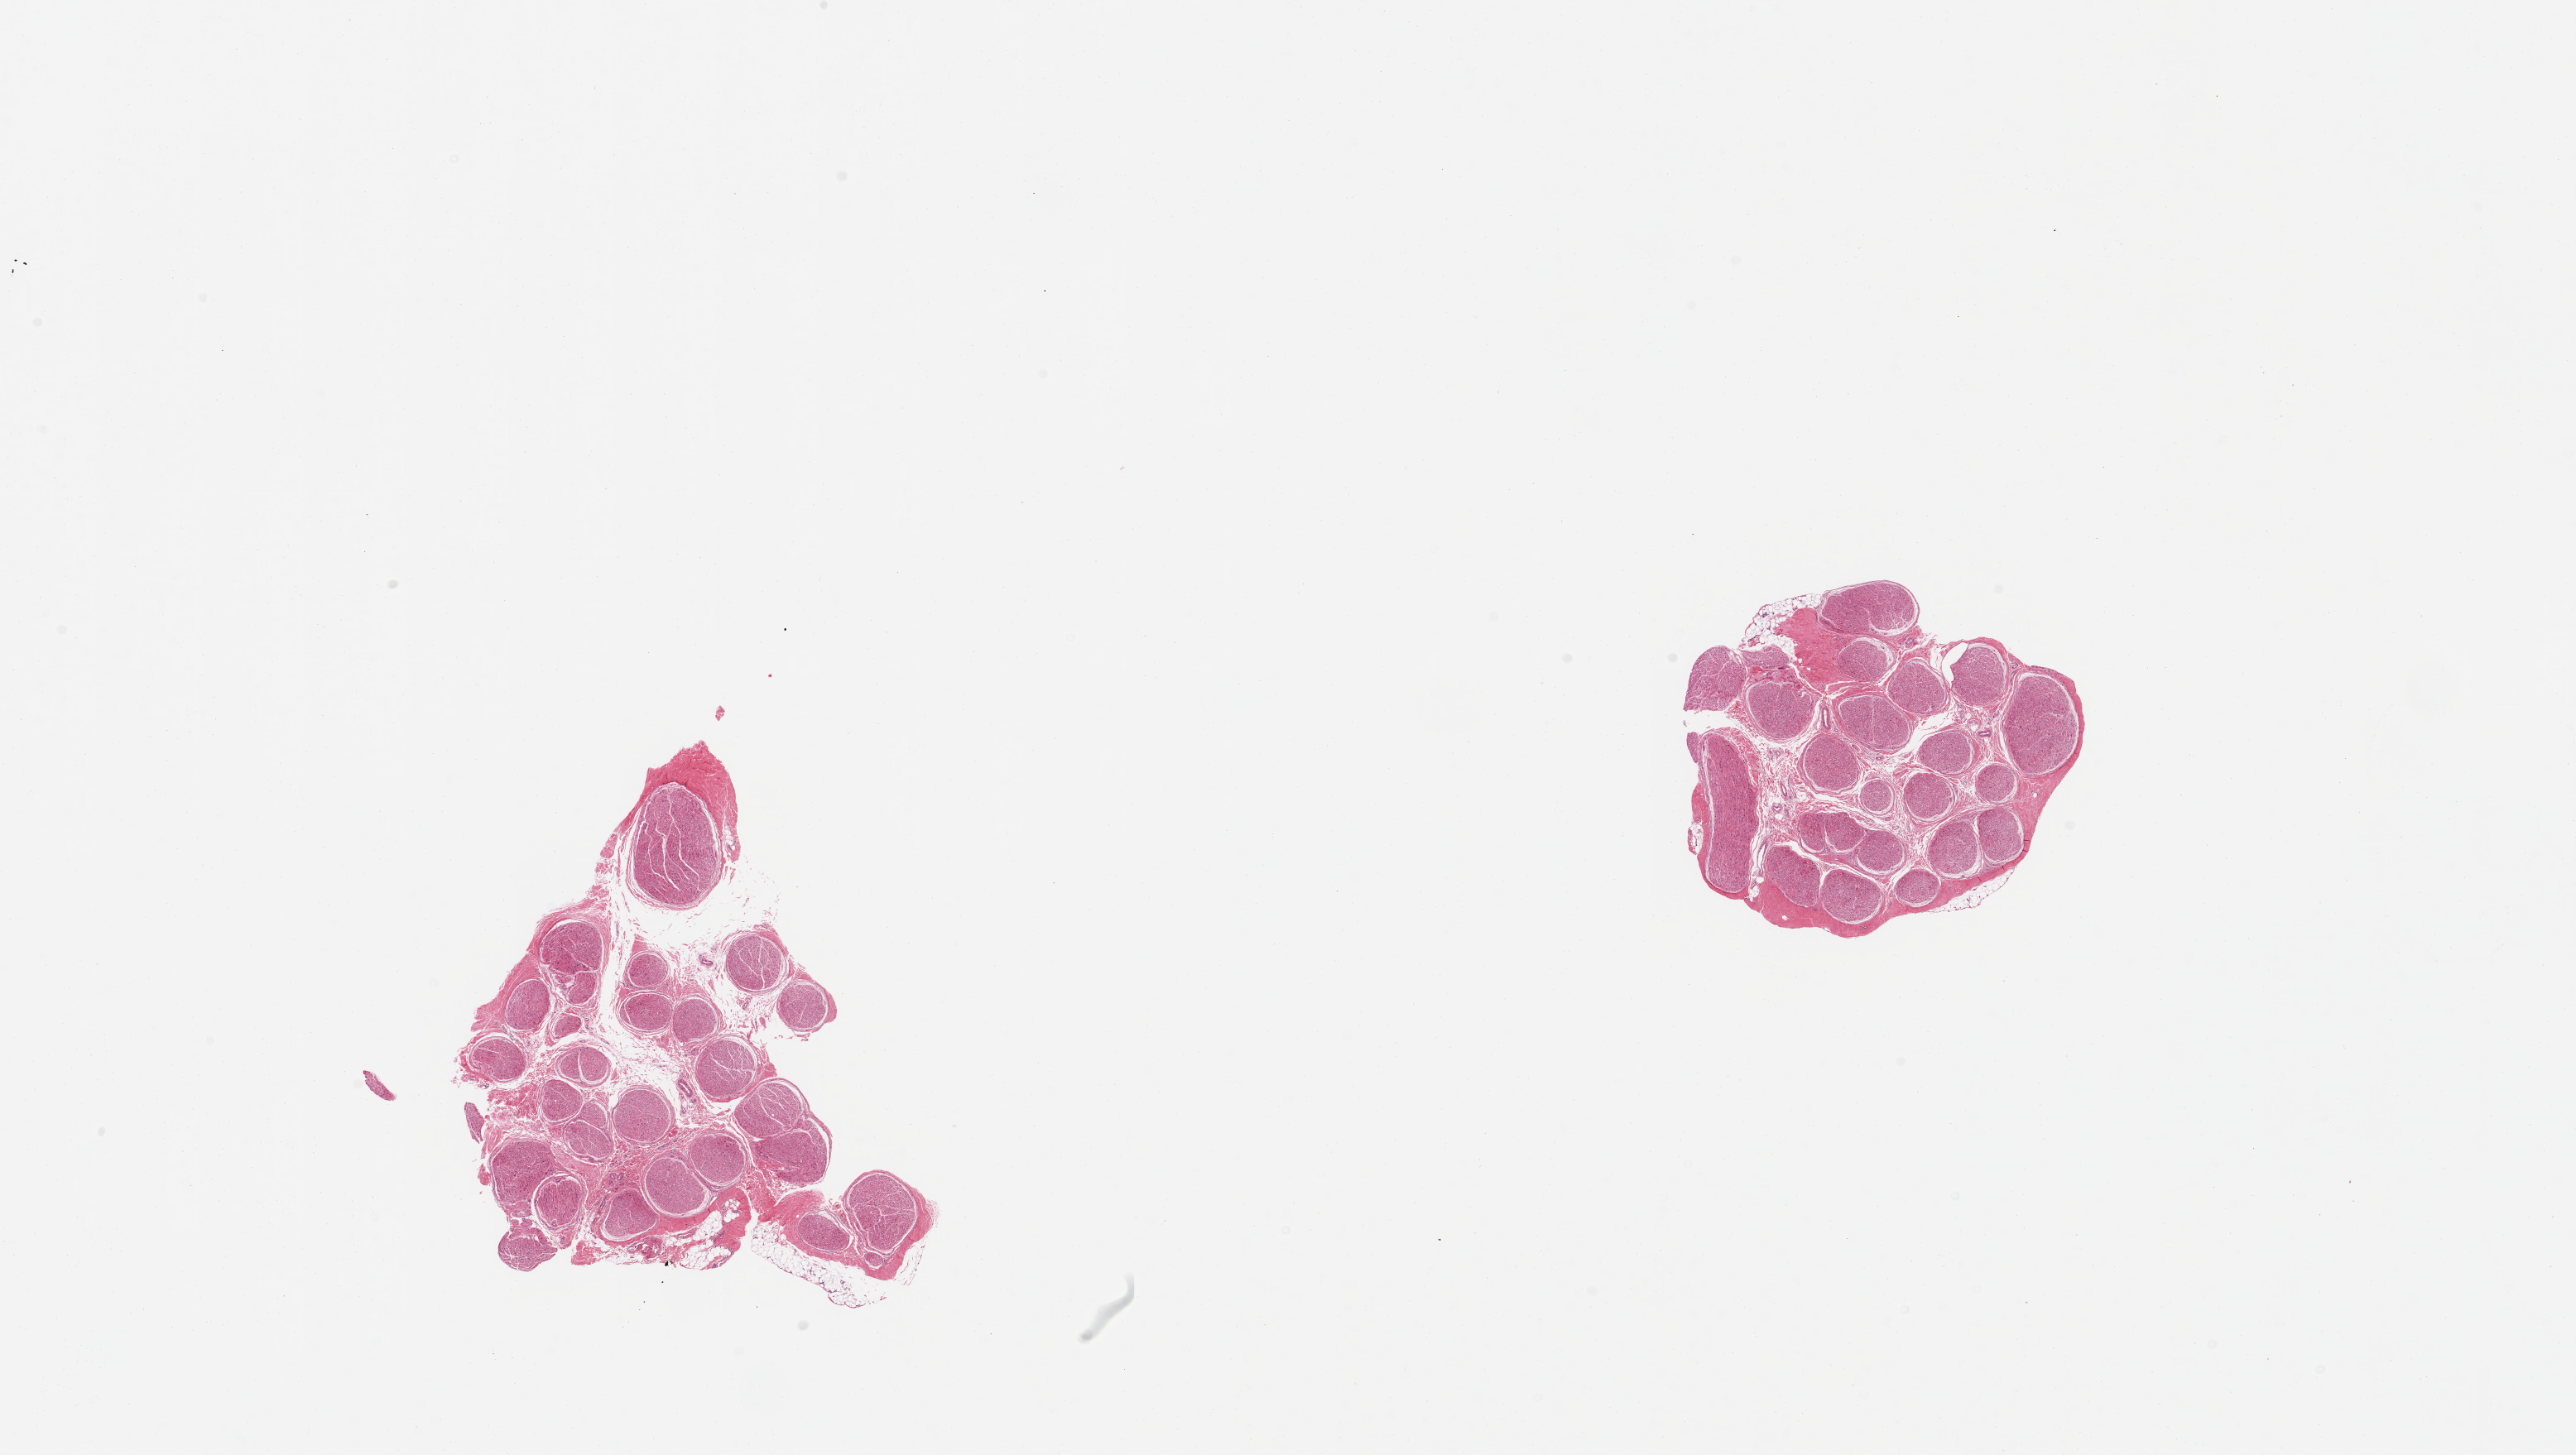
Whole-slide image, haematoxylin and eosin stain — a low-resolution overview of the entire scanned area, about 24.6 x 13.9 mm (slide scanned at 20x), PAXgene-fixed paraffin-embedded (PFPE) section, section of tibial nerve (target tissue), tissue donor sample. Donor: male.
• pathologist's review note for this sample: 2 pieces; well trimmed, trivial attachment of fat